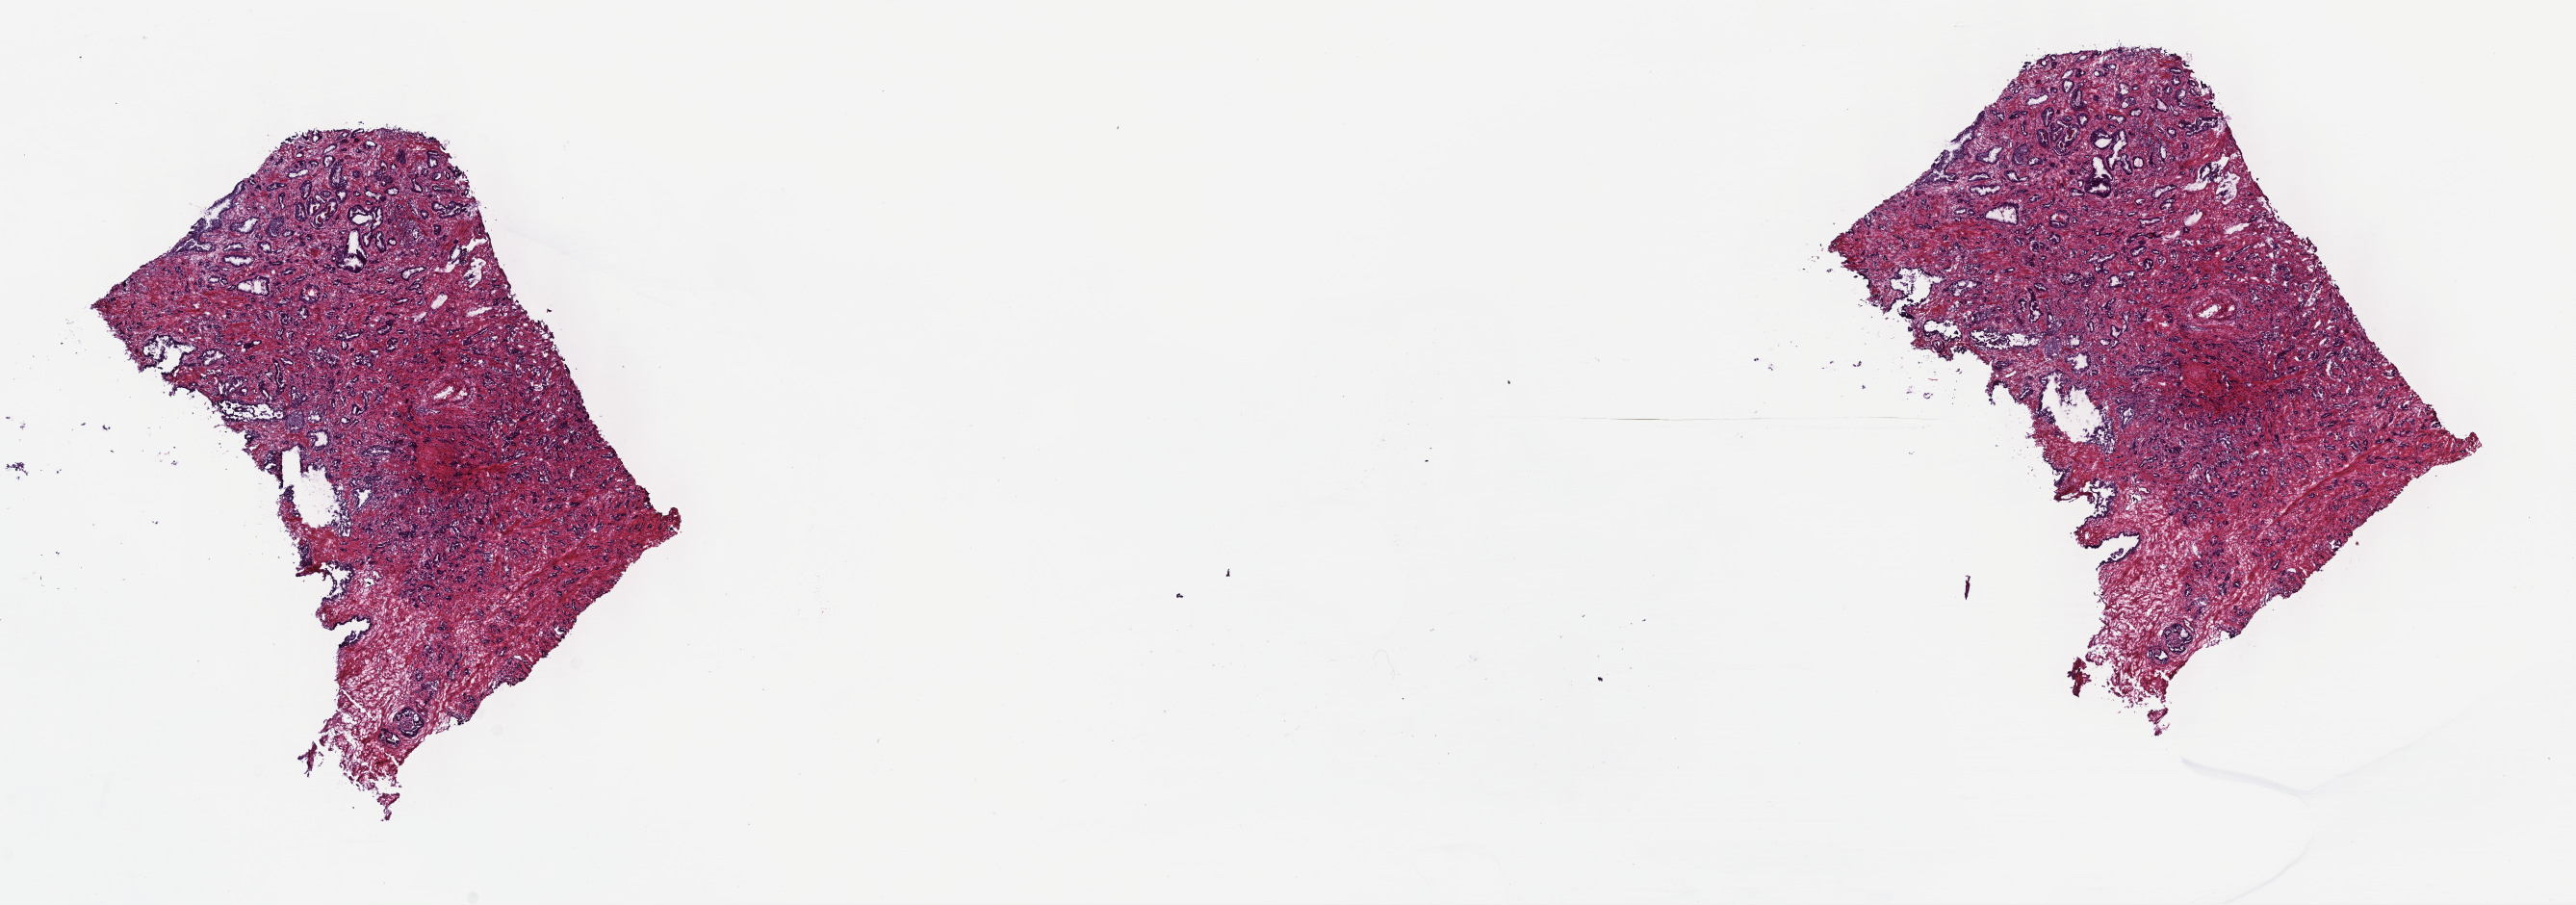
Digitized H&E tissue section (whole slide), shown as a low-resolution overview of the whole scanned area (about 21.6 x 7.6 mm, slide scanned at 40x), frozen section from the top of the tissue portion, primary tumour sample from the prostate. Male patient; age at initial diagnosis 68 years. Gleason score: 7 (3+4). Slide review estimates, as recorded: tumour cells 70%, tumour nuclei 70%, normal cells 0%, stromal cells 30%, necrosis 0%. Inflammatory infiltration, as recorded: lymphocyte infiltration 40%, monocyte infiltration 20%, neutrophil infiltration 20%.
Lymph nodes positive (case pathology): 0 of 6 examined. Histologic diagnosis: Adenocarcinoma, NOS (prostate gland). Laterality: bilateral.